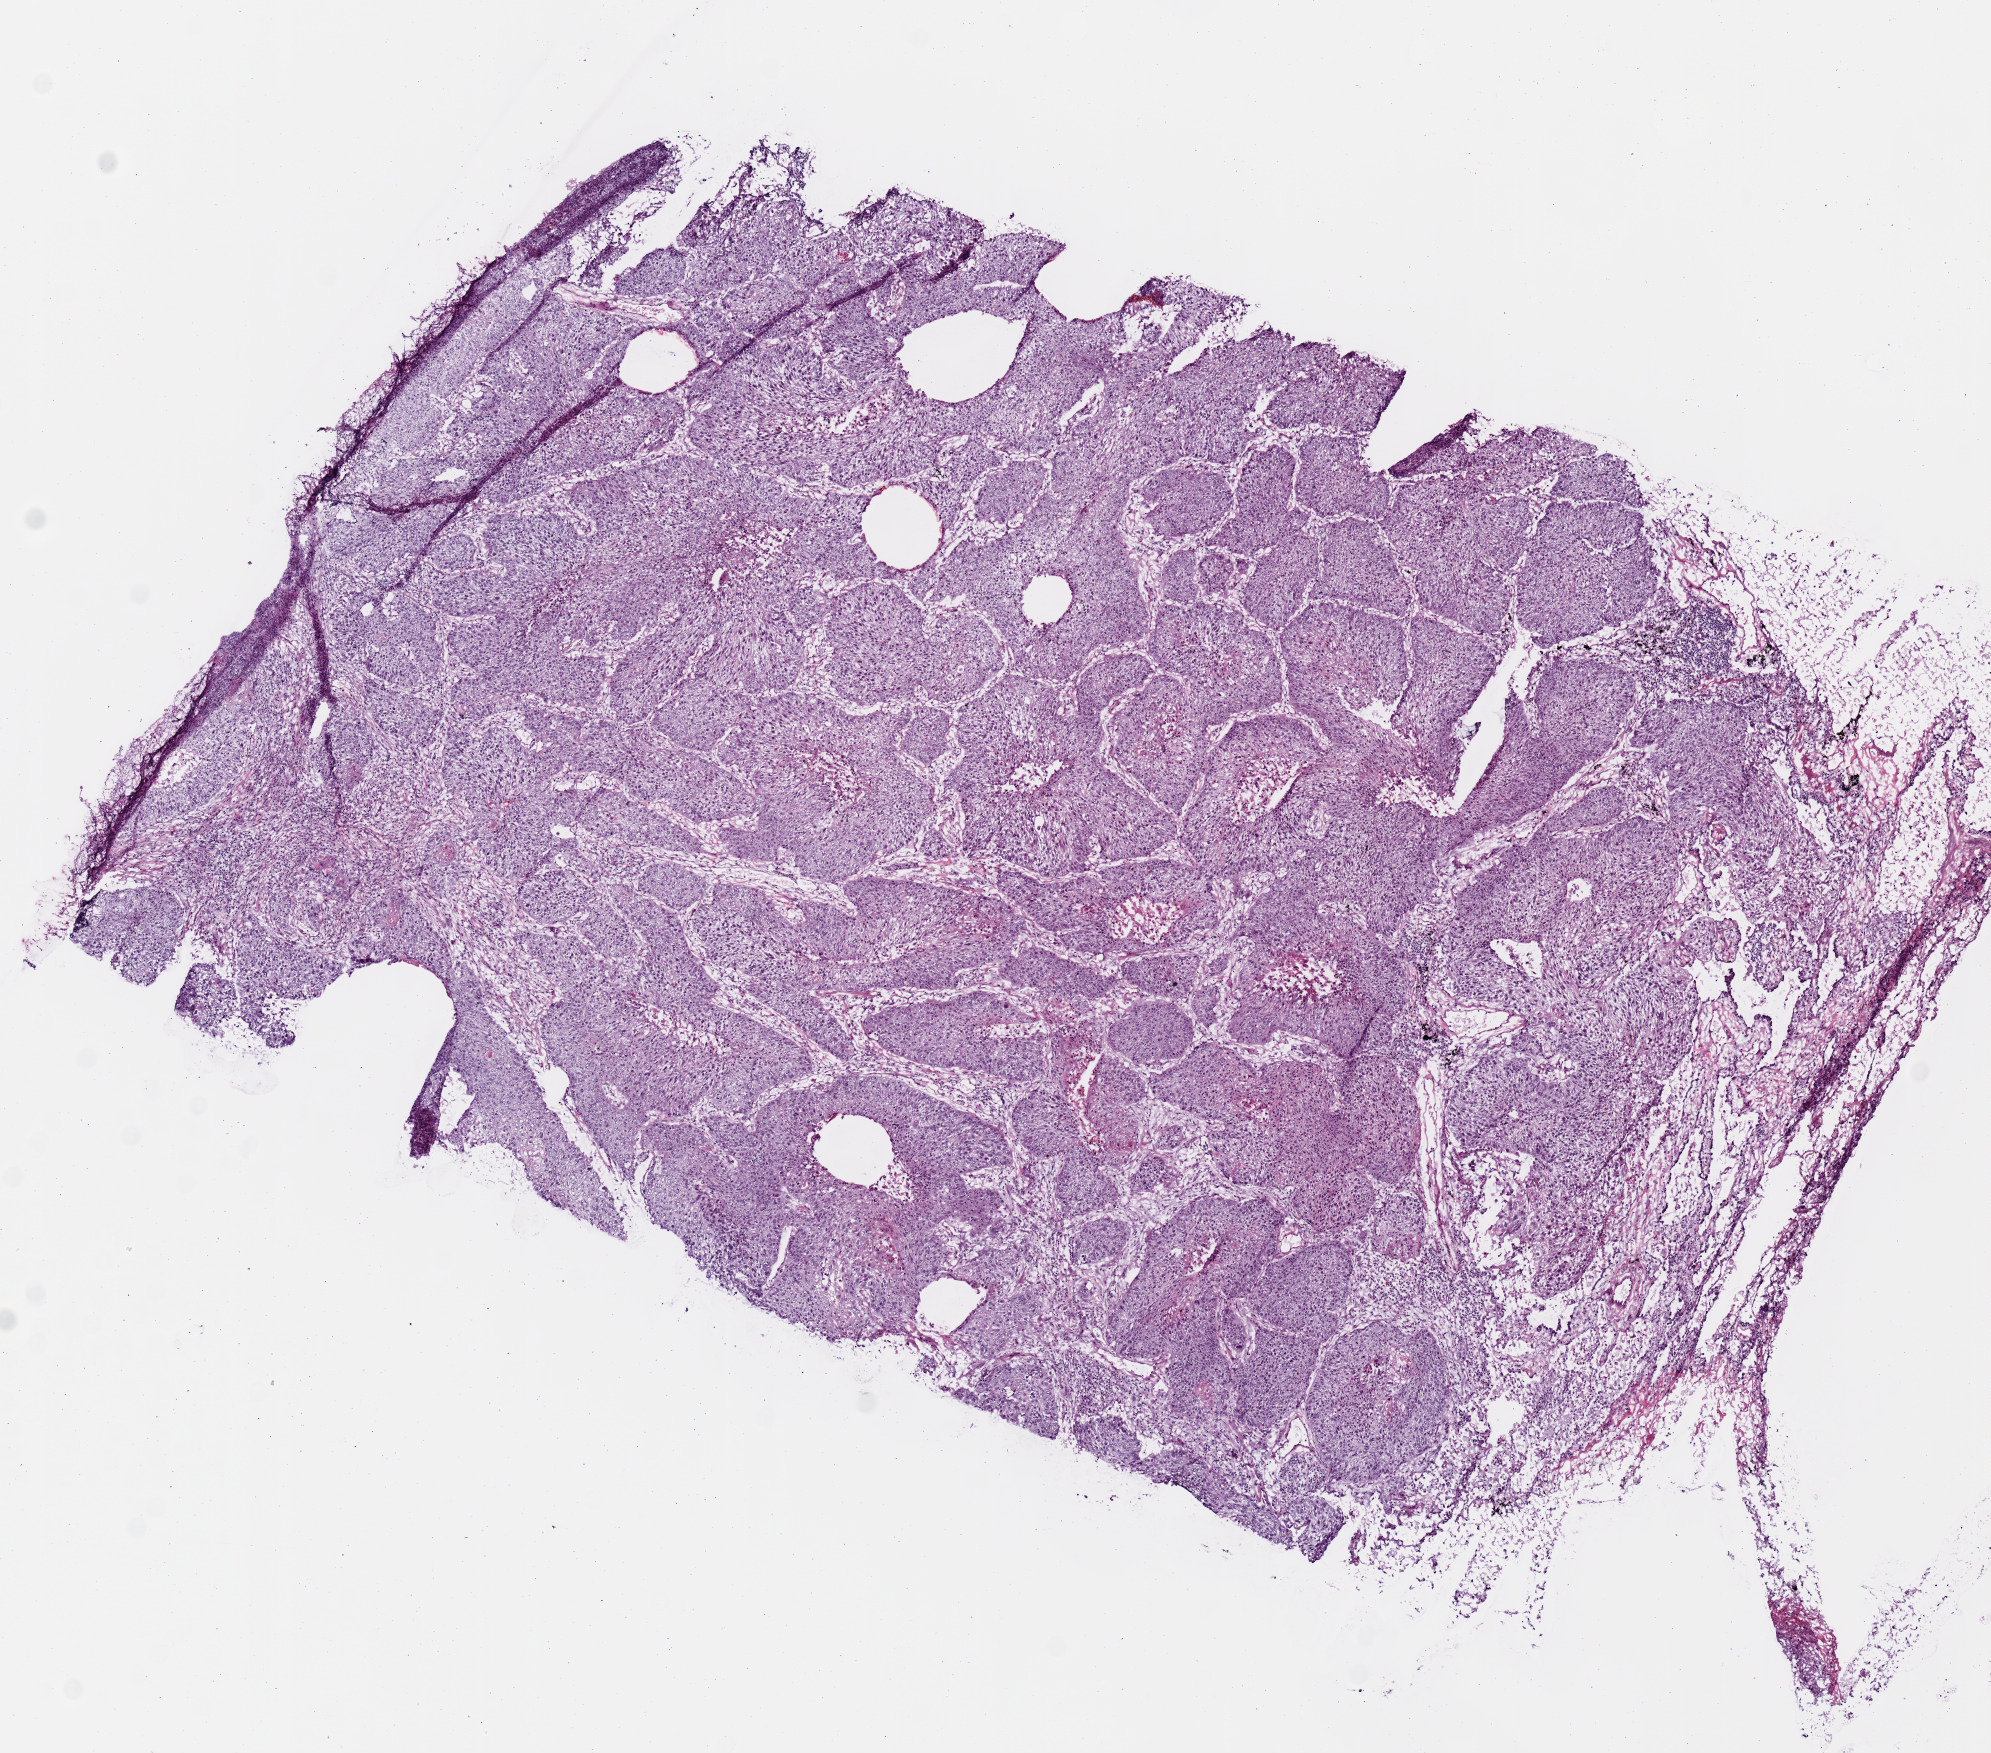
H&E whole-slide image — a low-resolution overview of the entire scanned area, about 7.9 x 6.9 mm. Frozen section from the top of the tissue portion. Primary tumour sample from the lung. Male patient; age at initial diagnosis 74 years. Slide review estimates, as recorded: tumour nuclei 80%, necrosis 2%.
• AJCC pathologic stage: IB (7th edition)
• laterality: left
• pathologic diagnosis: Squamous cell carcinoma, NOS